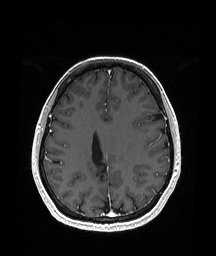
Brain MRI from a brain-tumour surgery series, one axial slice. Slice 73 of 151 in the series (ordered by position). T1-weighted post-contrast. 1.05 mm slice thickness. 216 × 256 image matrix, field of view 211 × 250 mm. From the clinical record (not read from this slice): histopathology: Oligodendroglioma; WHO grade: 2; IDH mutation: yes; tumour location: Right Parietal.
Structures marked on this image (manually delineated by an expert):
- previous resection cavity: bounding box (x1, y1, x2, y2) in pixels: (94, 155, 109, 175)